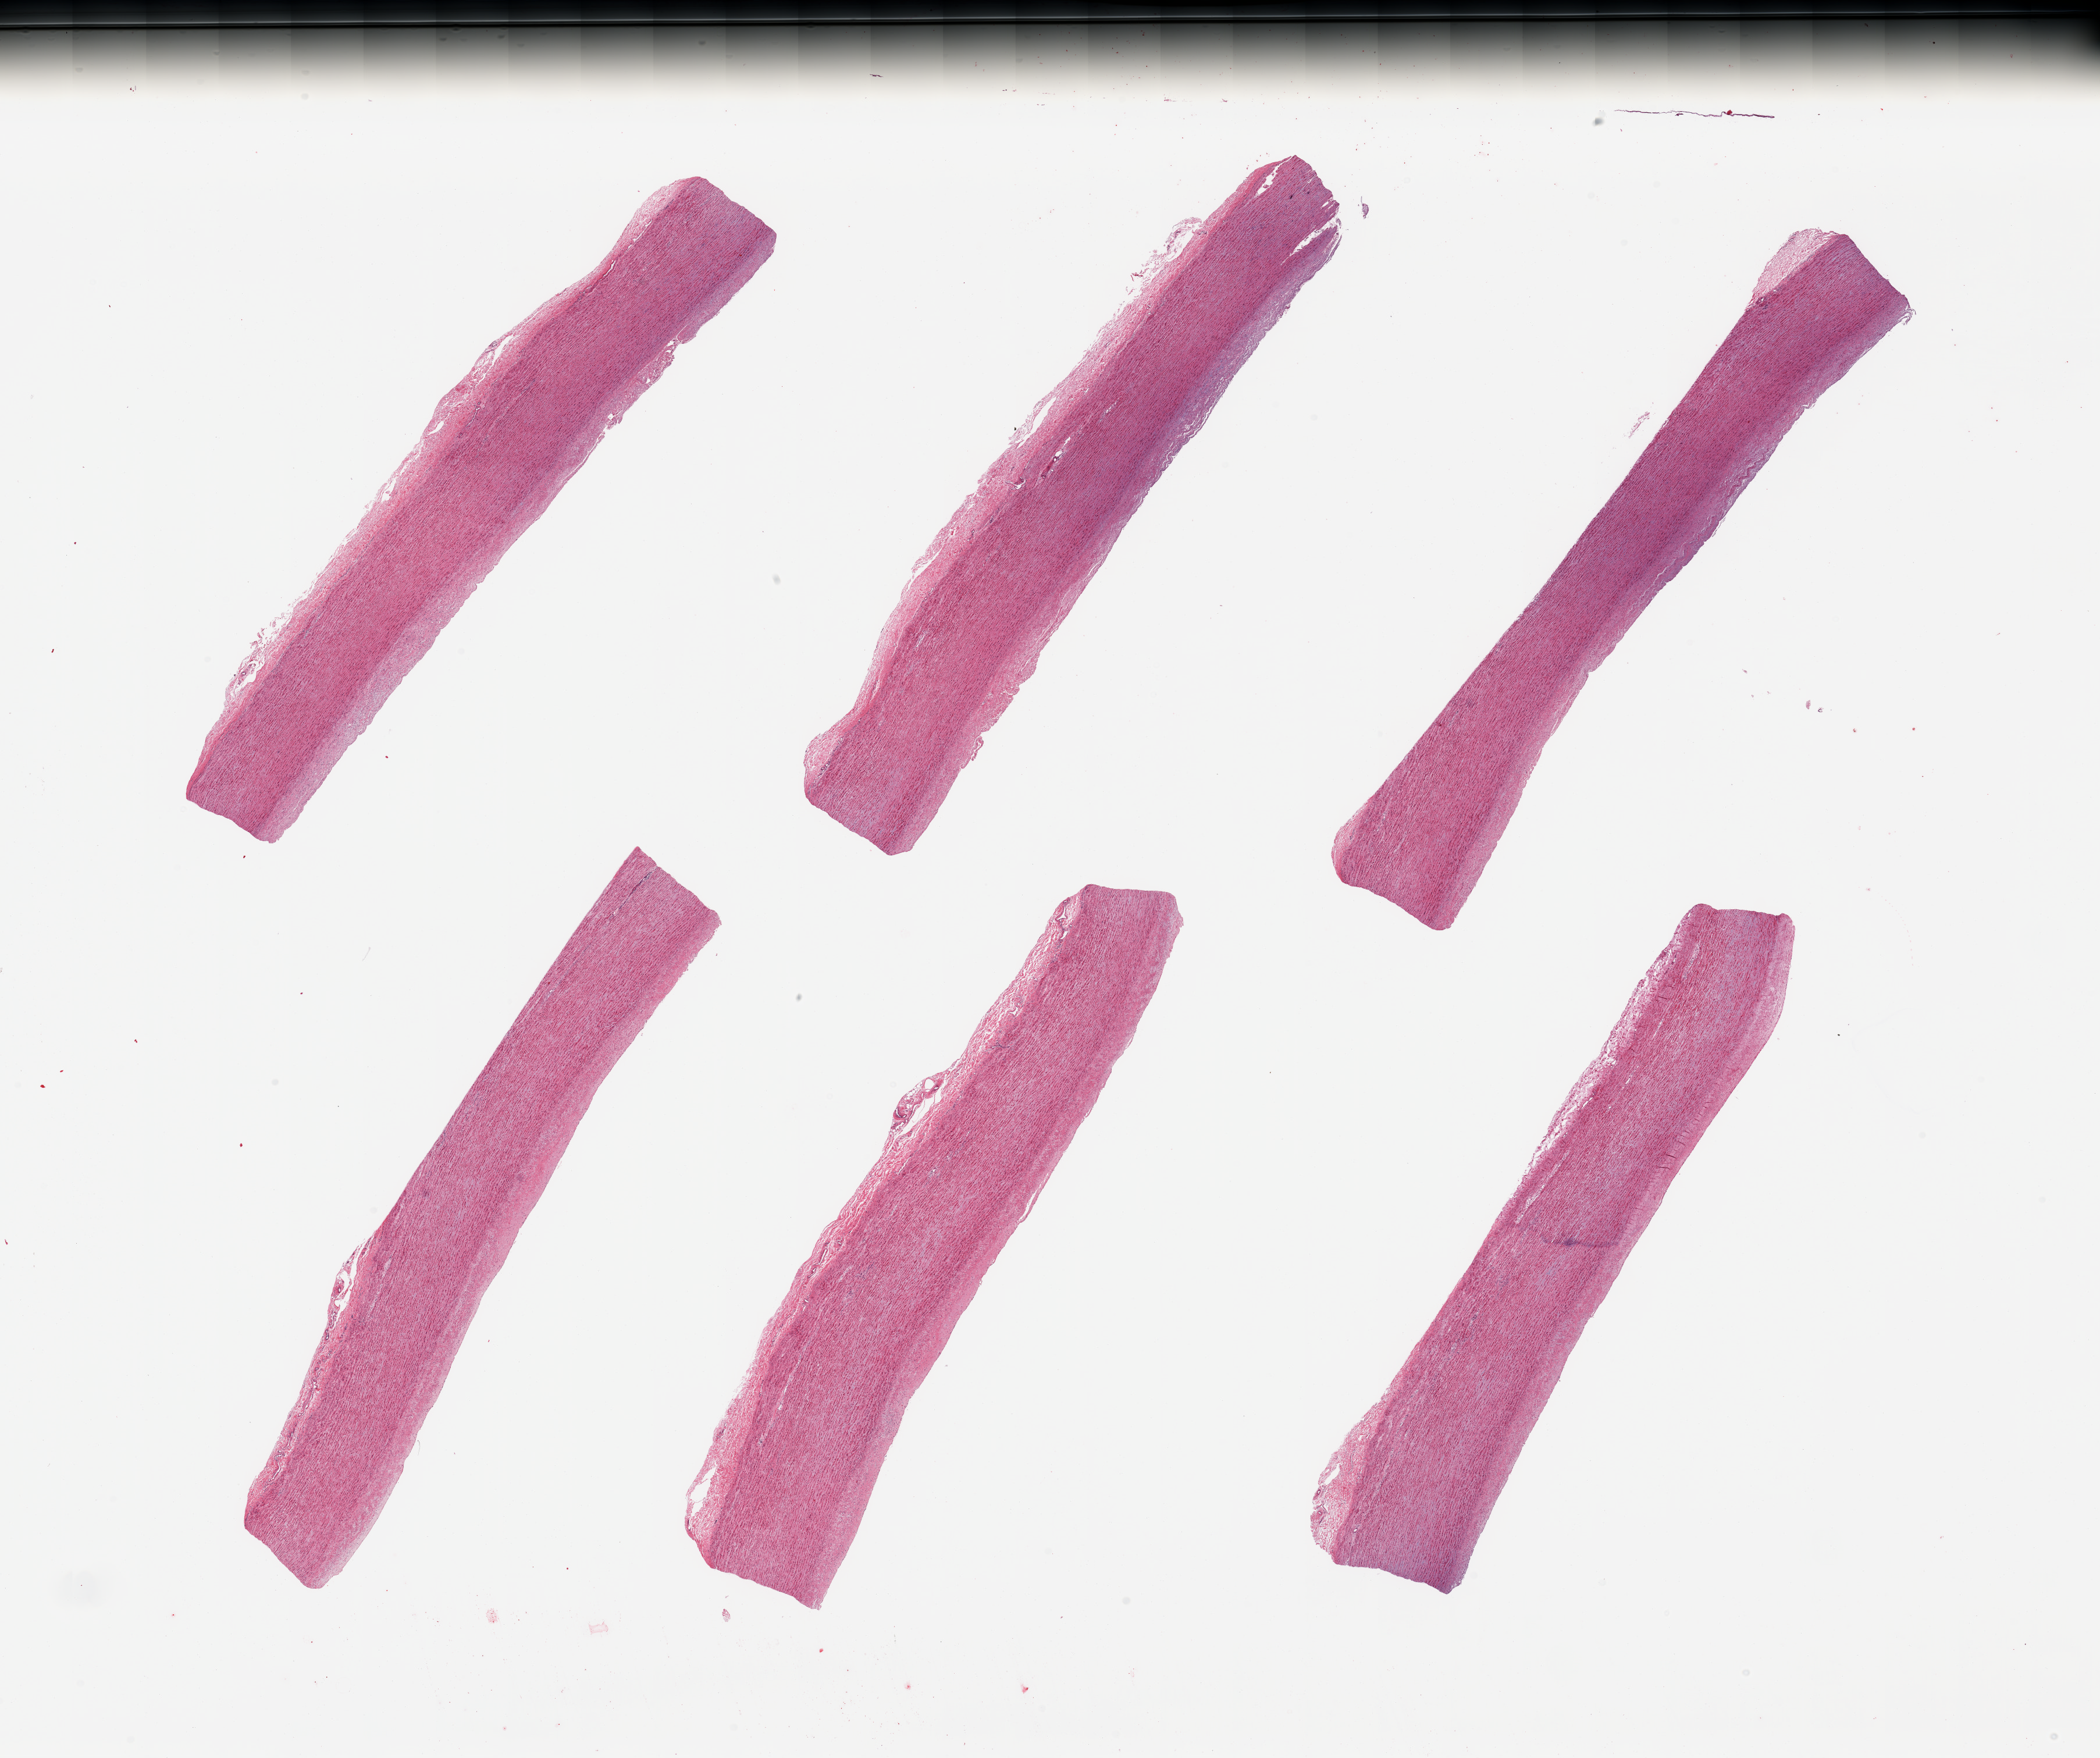
Whole-slide image, hematoxylin and eosin (H&E) stain — a low-resolution overview of the entire scanned area, about 28.5 x 23.9 mm (slide scanned at 20x), PAXgene-fixed, paraffin-embedded tissue, section of aorta (target tissue), tissue donor sample. Donor sex: male.
• reviewer comment on this tissue sample: 6 pieces, atherosis up to ~0.3mm